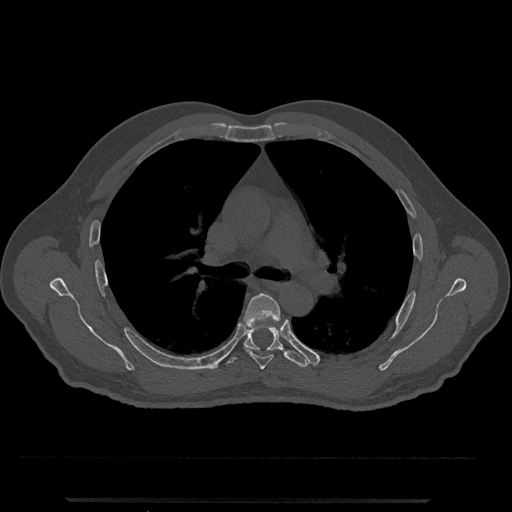
CT including the spine, one axial slice. Position 767 of 797 along the scan axis. Reconstruction kernel Br40s/3. 120 kVp. Bone window (W 1800 / L 400 HU). 0.5 mm slice thickness. 512 × 512 image matrix, field of view 419 × 419 mm. Male patient, age 63 years. Case-level facts recorded for this patient, not image findings: primary cancer: prostate.
Structures marked on this image (semi-automatic segmentation, software-assisted and operator-edited):
- T5 vertebra: bounding box <244,293,281,370> (left, top, right, bottom; pixels)
- T6 vertebra: <226,321,308,368>